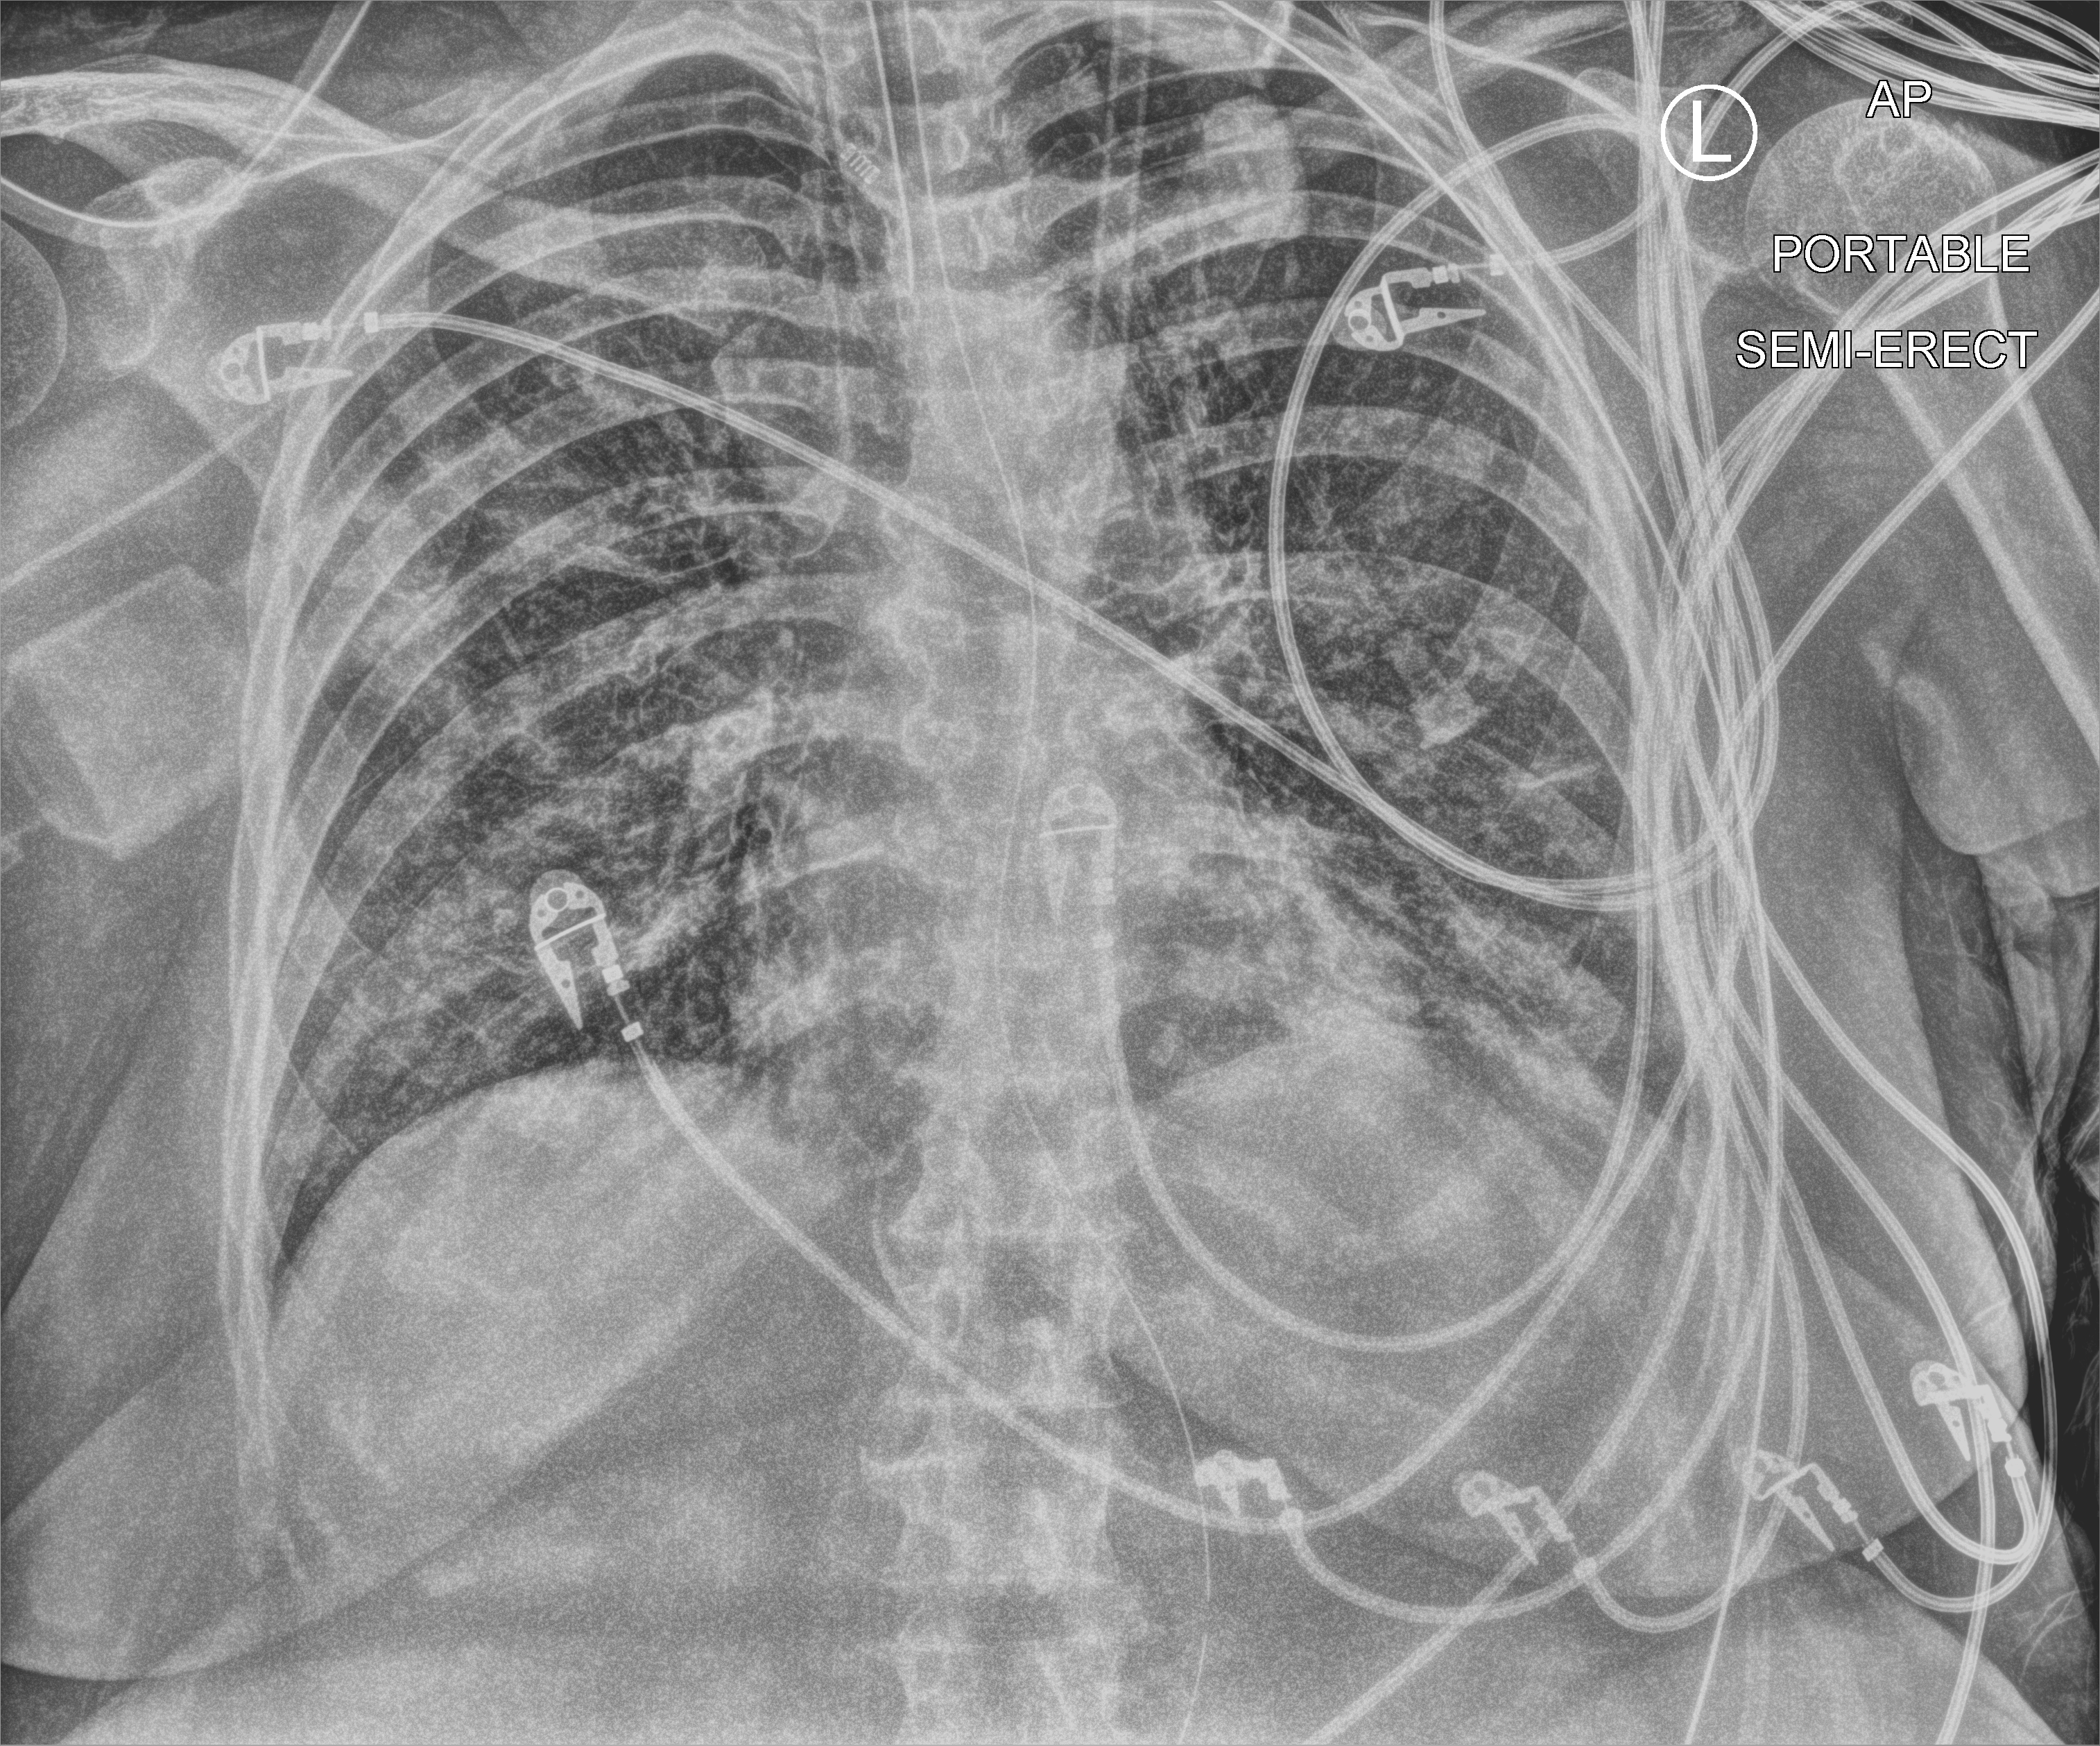
Bedside chest radiograph (computed radiography), anteroposterior (AP) projection. Female patient hospitalised with COVID-19, age 75–90 years.
Admission-level facts for this patient (not findings on this image; timing relative to this image not recorded): other chronic lung disease (admission record): no.